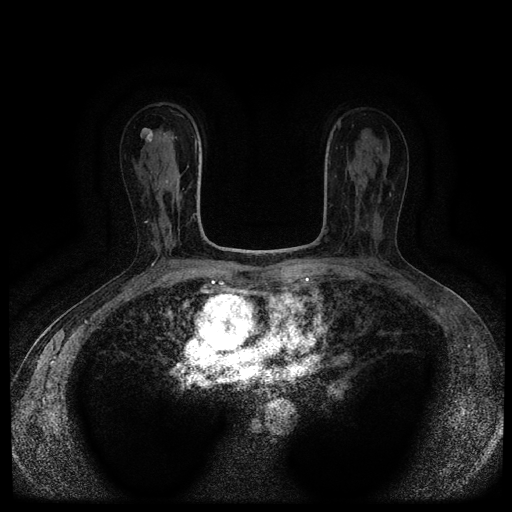
Breast MRI (dynamic contrast-enhanced, multi-phase), one axial slice; position 60 of 116 along the scan axis; dynamic contrast-enhanced series, time point 2 of 5 at this slice position (early post-contrast); 1.5 T; TE 2.7 ms, TR 5.4 ms; 2 mm slice thickness; 512 × 512 image matrix. Female patient, age 63 years.
Structures marked on this image (semi-automatically segmented with operator editing):
- breast lesion (labelled benign in the annotation): bounding box <140,128,153,142> (left, top, right, bottom; pixels)